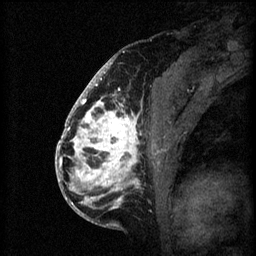
Breast MRI (dynamic contrast-enhanced), one sagittal slice; position 34 of 60 along the scan axis; 3 images stored at this slice position (order not interpretable as contrast timing); 1.5 T; TE 4.2 ms, TR 8.2 ms; 2 mm slice thickness; 256 × 256 image matrix. Female patient, age 41 years.
Annotated regions visible in this slice (semi-automatically segmented with operator editing):
- analysis volume of interest (the breast-tissue region the enhancement analysis was run in; not a lesion): box from (x=72, y=108) to (x=176, y=205) px
- tumour enhancement mask (voxels above the 70 % enhancement threshold inside the analysis volume of interest): (x=72, y=108)–(x=140, y=205)